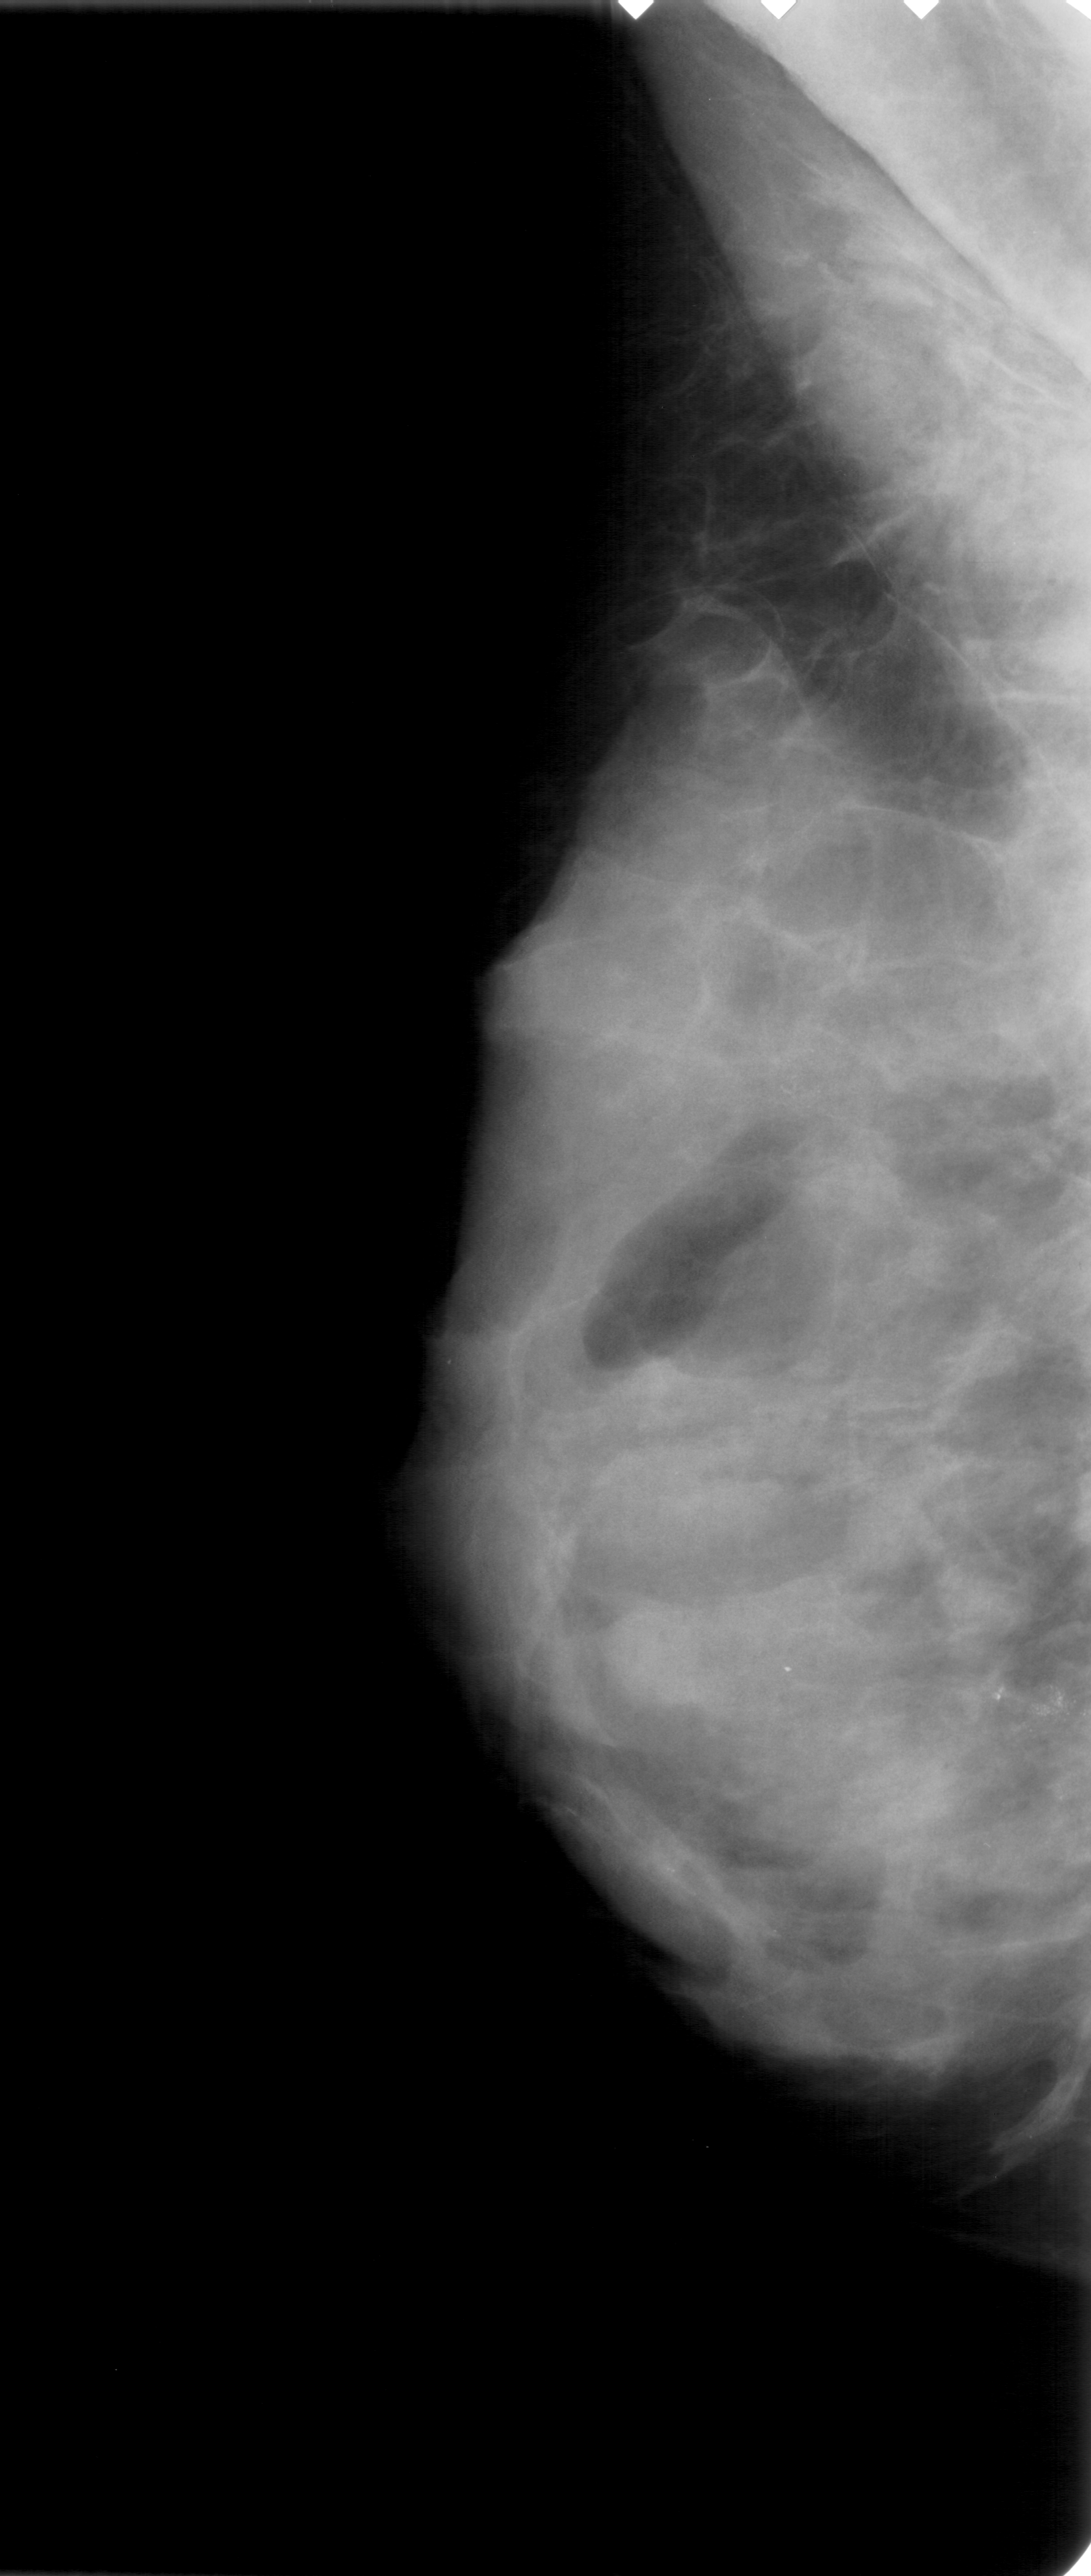
Mammogram (digitized film); left breast; mediolateral oblique (MLO) view; 1091 × 2576 image matrix.
Marked abnormalities (boxes around the expert regions of interest):
- Finding 1 of 2: calcifications, morphology pleomorphic, distribution clustered; BI-RADS assessment category 4; subtlety rating 3 on a 1 (subtle) to 5 (obvious) scale; pathology (as recorded): malignant: bounding box <760,1038,846,1124> (left, top, right, bottom; pixels)
- Finding 2 of 2: calcifications, morphology pleomorphic, distribution clustered; BI-RADS assessment category 4; pathology result (as recorded, not read from the image): malignant: <1002,1681,1091,1751>